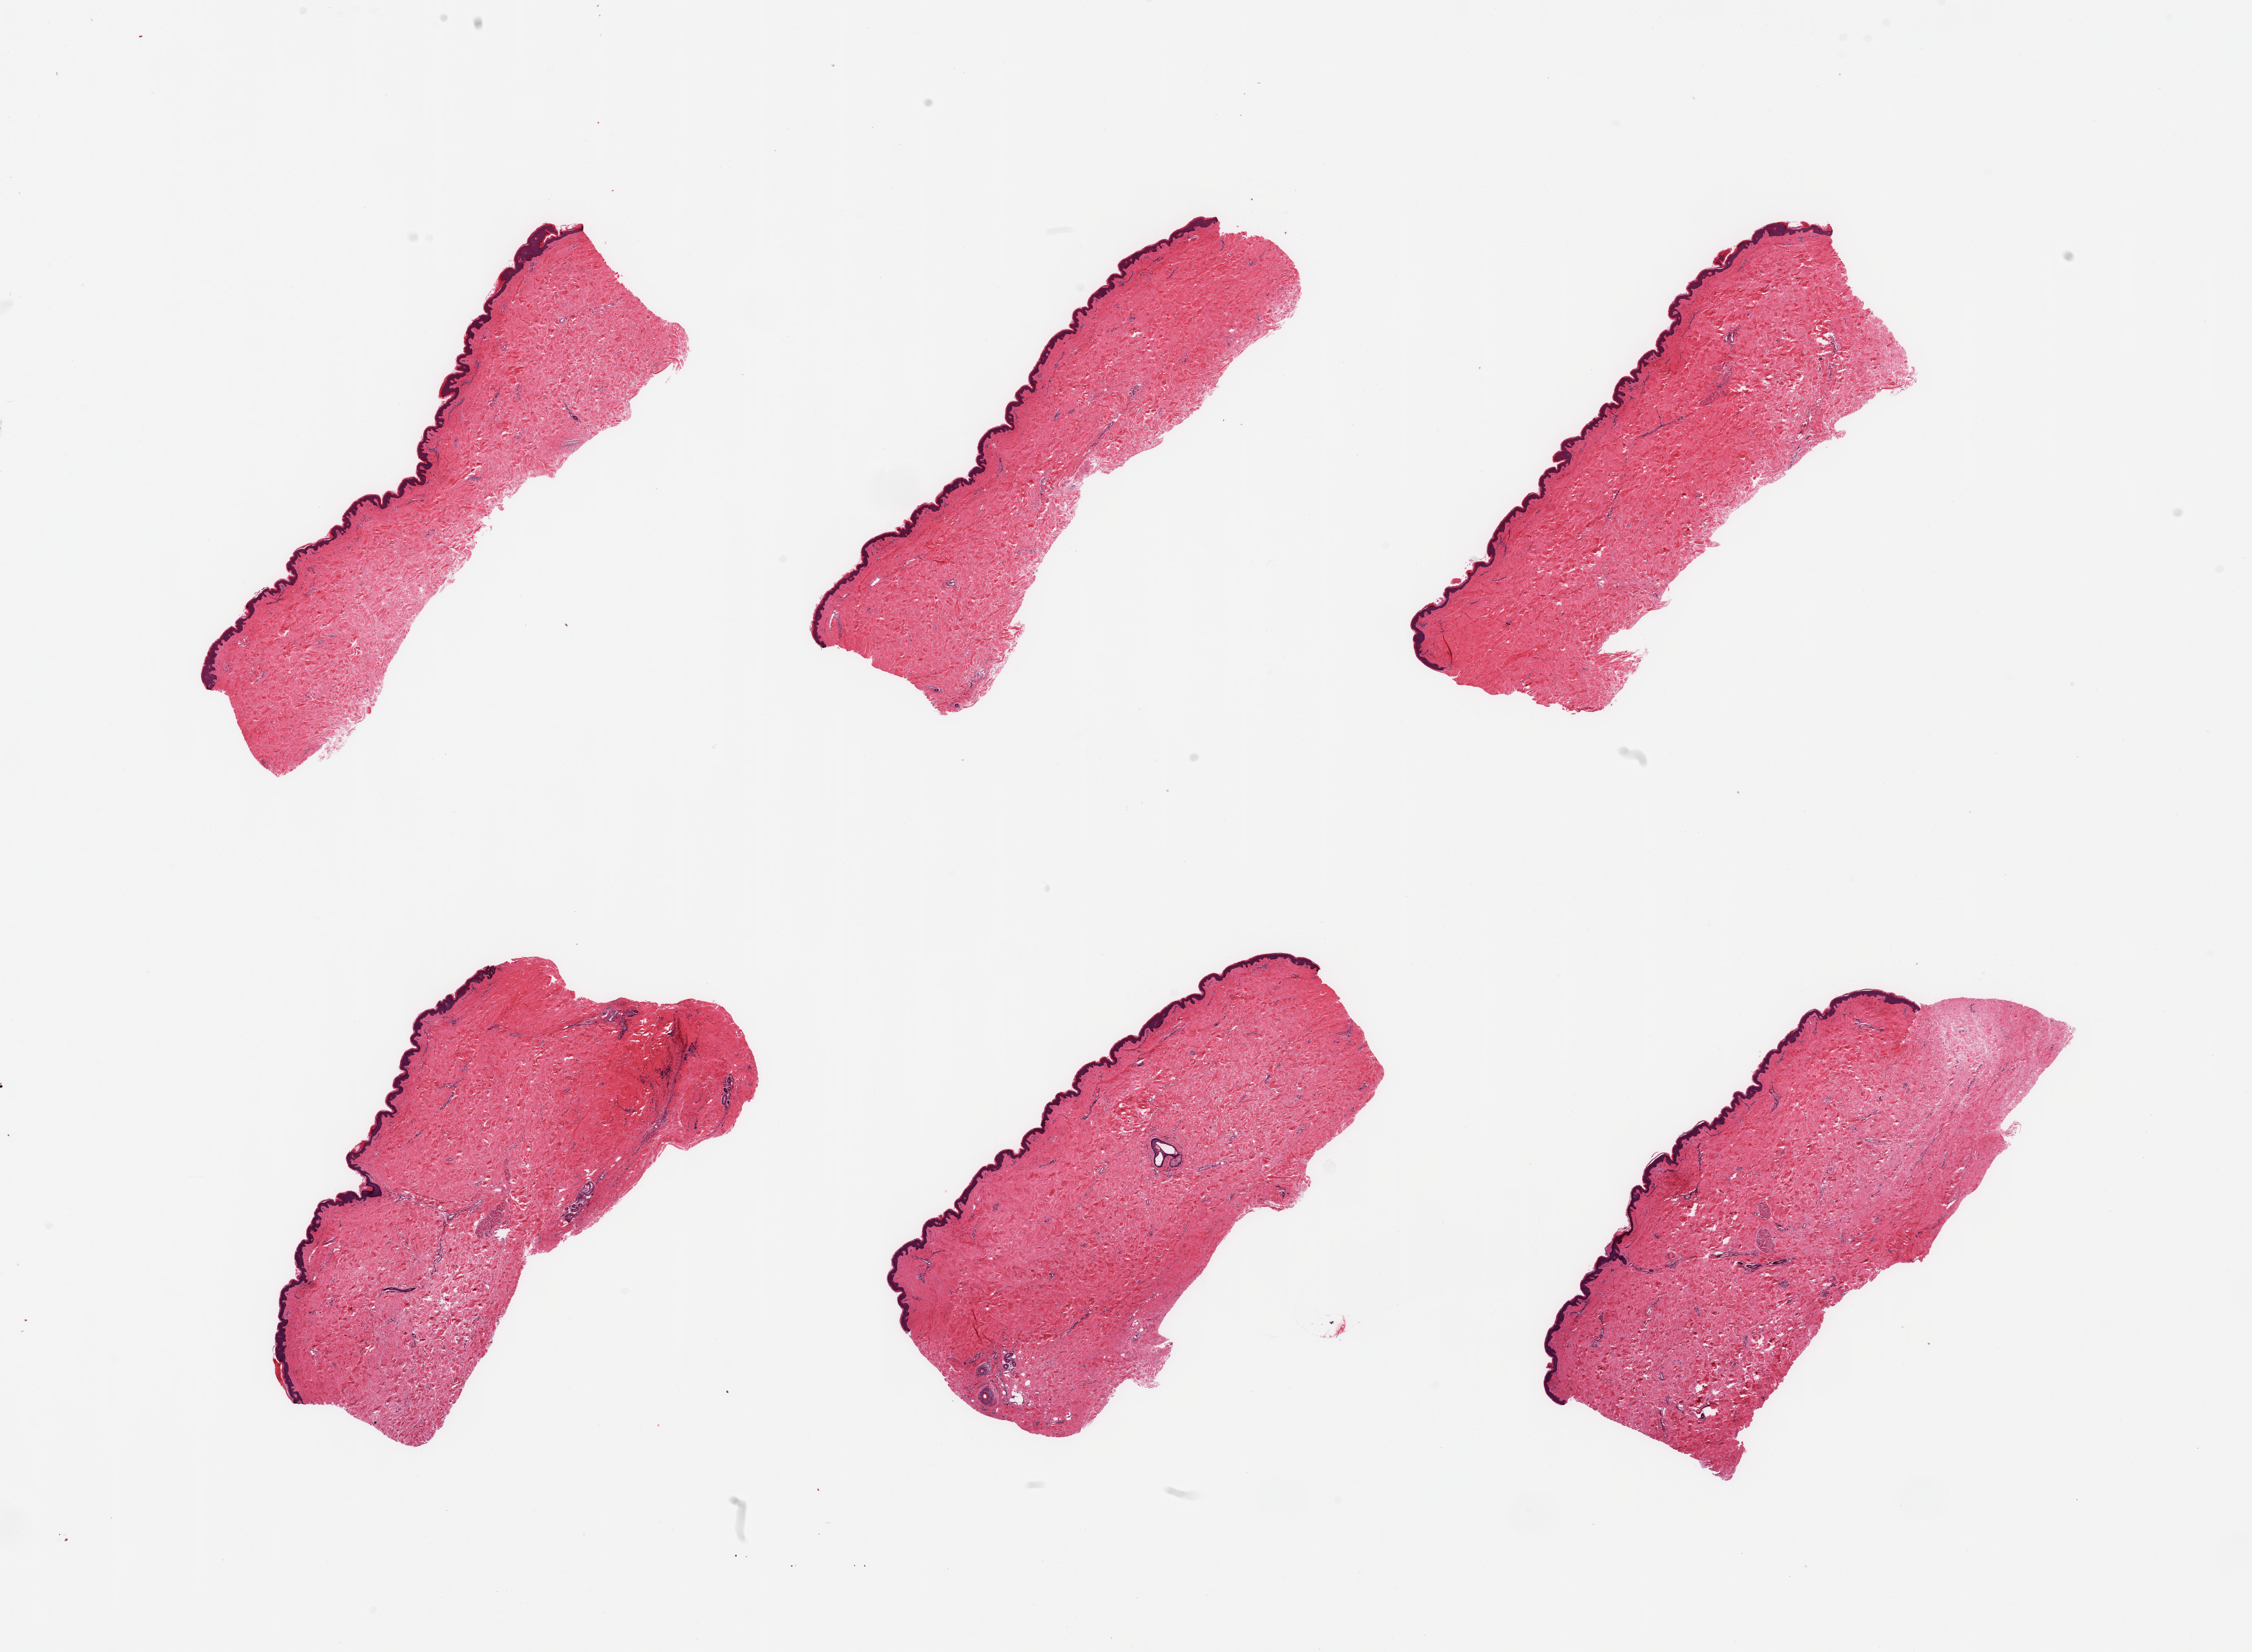
Haematoxylin and eosin whole-slide image, brightfield — shown as a low-resolution overview of the whole scanned area (about 27.6 x 20.2 mm, from a 20x scan), PAXgene-fixed paraffin-embedded (PFPE) section, section of skin of suprapubic region (target tissue), donor tissue sample.
* reviewer comment on this tissue sample: 6 pieces; well trimmed; no dermal fat